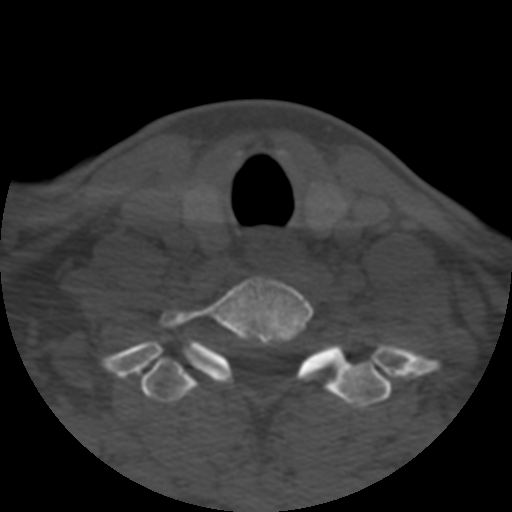
CT including the spine, one axial slice. Position 457 of 508 along the scan axis. Reconstruction kernel STANDARD. Bone window (W 1800 / L 400 HU). 1.25 mm slice thickness. 512 × 512 image matrix, field of view 160 × 160 mm. Patient age 57 years. From the clinical record (not read from this slice): primary cancer: prostate.
Structures marked on this image (semi-automatic segmentation, software-assisted and operator-edited):
- T1 vertebra: bounding box (x1, y1, x2, y2) in pixels: (141, 357, 391, 407)